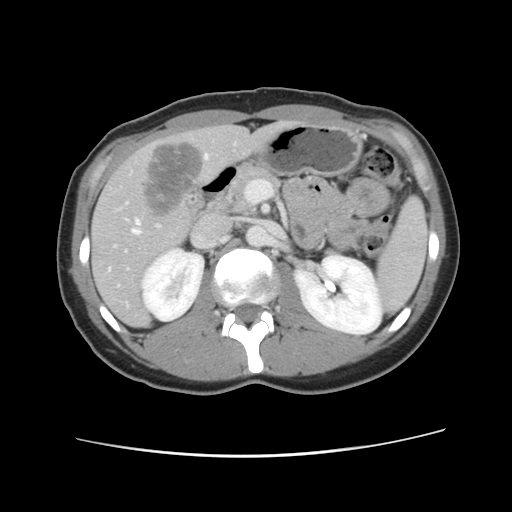
Contrast-enhanced abdominal CT, one axial slice; slice 50 of 134 in the series (ordered by position); 120 kVp; intravenous contrast given; soft-tissue window (W 400 / L 40 HU); 2.5 mm slice thickness; 512 × 512 image matrix, field of view 339 × 339 mm. Female patient, age 33 years. From the clinical record (not read from this slice): diagnosis: colorectal cancer liver metastases, imaged before liver resection; multiple liver metastases: yes; largest metastasis: 4.5 cm; disease in both lobes: yes.
Outlined on this slice (expert manual segmentation):
- hepatic veins: bounding box <133,155,209,235> (left, top, right, bottom; pixels)
- liver: <92,123,290,327>
- planned liver remnant (the part of the liver to remain after resection): <92,123,288,327>
- liver metastasis: <141,140,207,220>